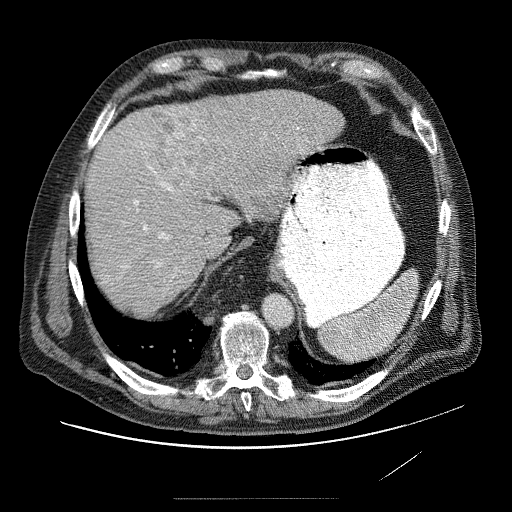
Contrast-enhanced abdominal CT (liver protocol), one axial slice; slice 61 of 89 in the series (ordered by position); soft-tissue window (W 400 / L 40 HU); 2.5 mm slice thickness; 512 × 512 image matrix, field of view 420 × 420 mm. From the clinical record (not read from this slice): diagnosis: hepatocellular carcinoma (patient treated with transarterial chemoembolisation; whether this scan precedes or follows treatment is not stated here); TNM stage (as recorded): Stage-IVA; Child-Pugh class: A; tumour differentiation: moderately differentiated.
Annotated regions visible in this slice (semi-automatically segmented with operator editing):
- liver parenchyma outside the tumour (the mass and vessels are separate outlines, so this box may not span the whole liver): box from (x=86, y=90) to (x=346, y=300) px
- mass: (x=151, y=100)–(x=280, y=221)
- liver vessels: (x=115, y=116)–(x=333, y=276)